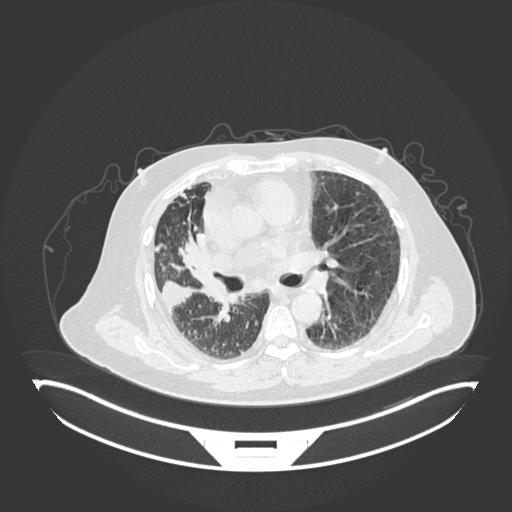
Chest CT, one axial slice. Reconstruction kernel B30f. Lung window (W 1500 / L -600 HU). 1 mm slice thickness. 512 × 512 image matrix, field of view 500 × 500 mm. Male patient, age 69 years. From the clinical record (not read from this slice): clinical TNM (as recorded): T4 N3 M1.
Outlined on this slice (rectangle marked by the reading radiologist):
- lung tumour (recorded histology: adenocarcinoma): bounding box [x1, y1, x2, y2] px = [174, 231, 212, 275]